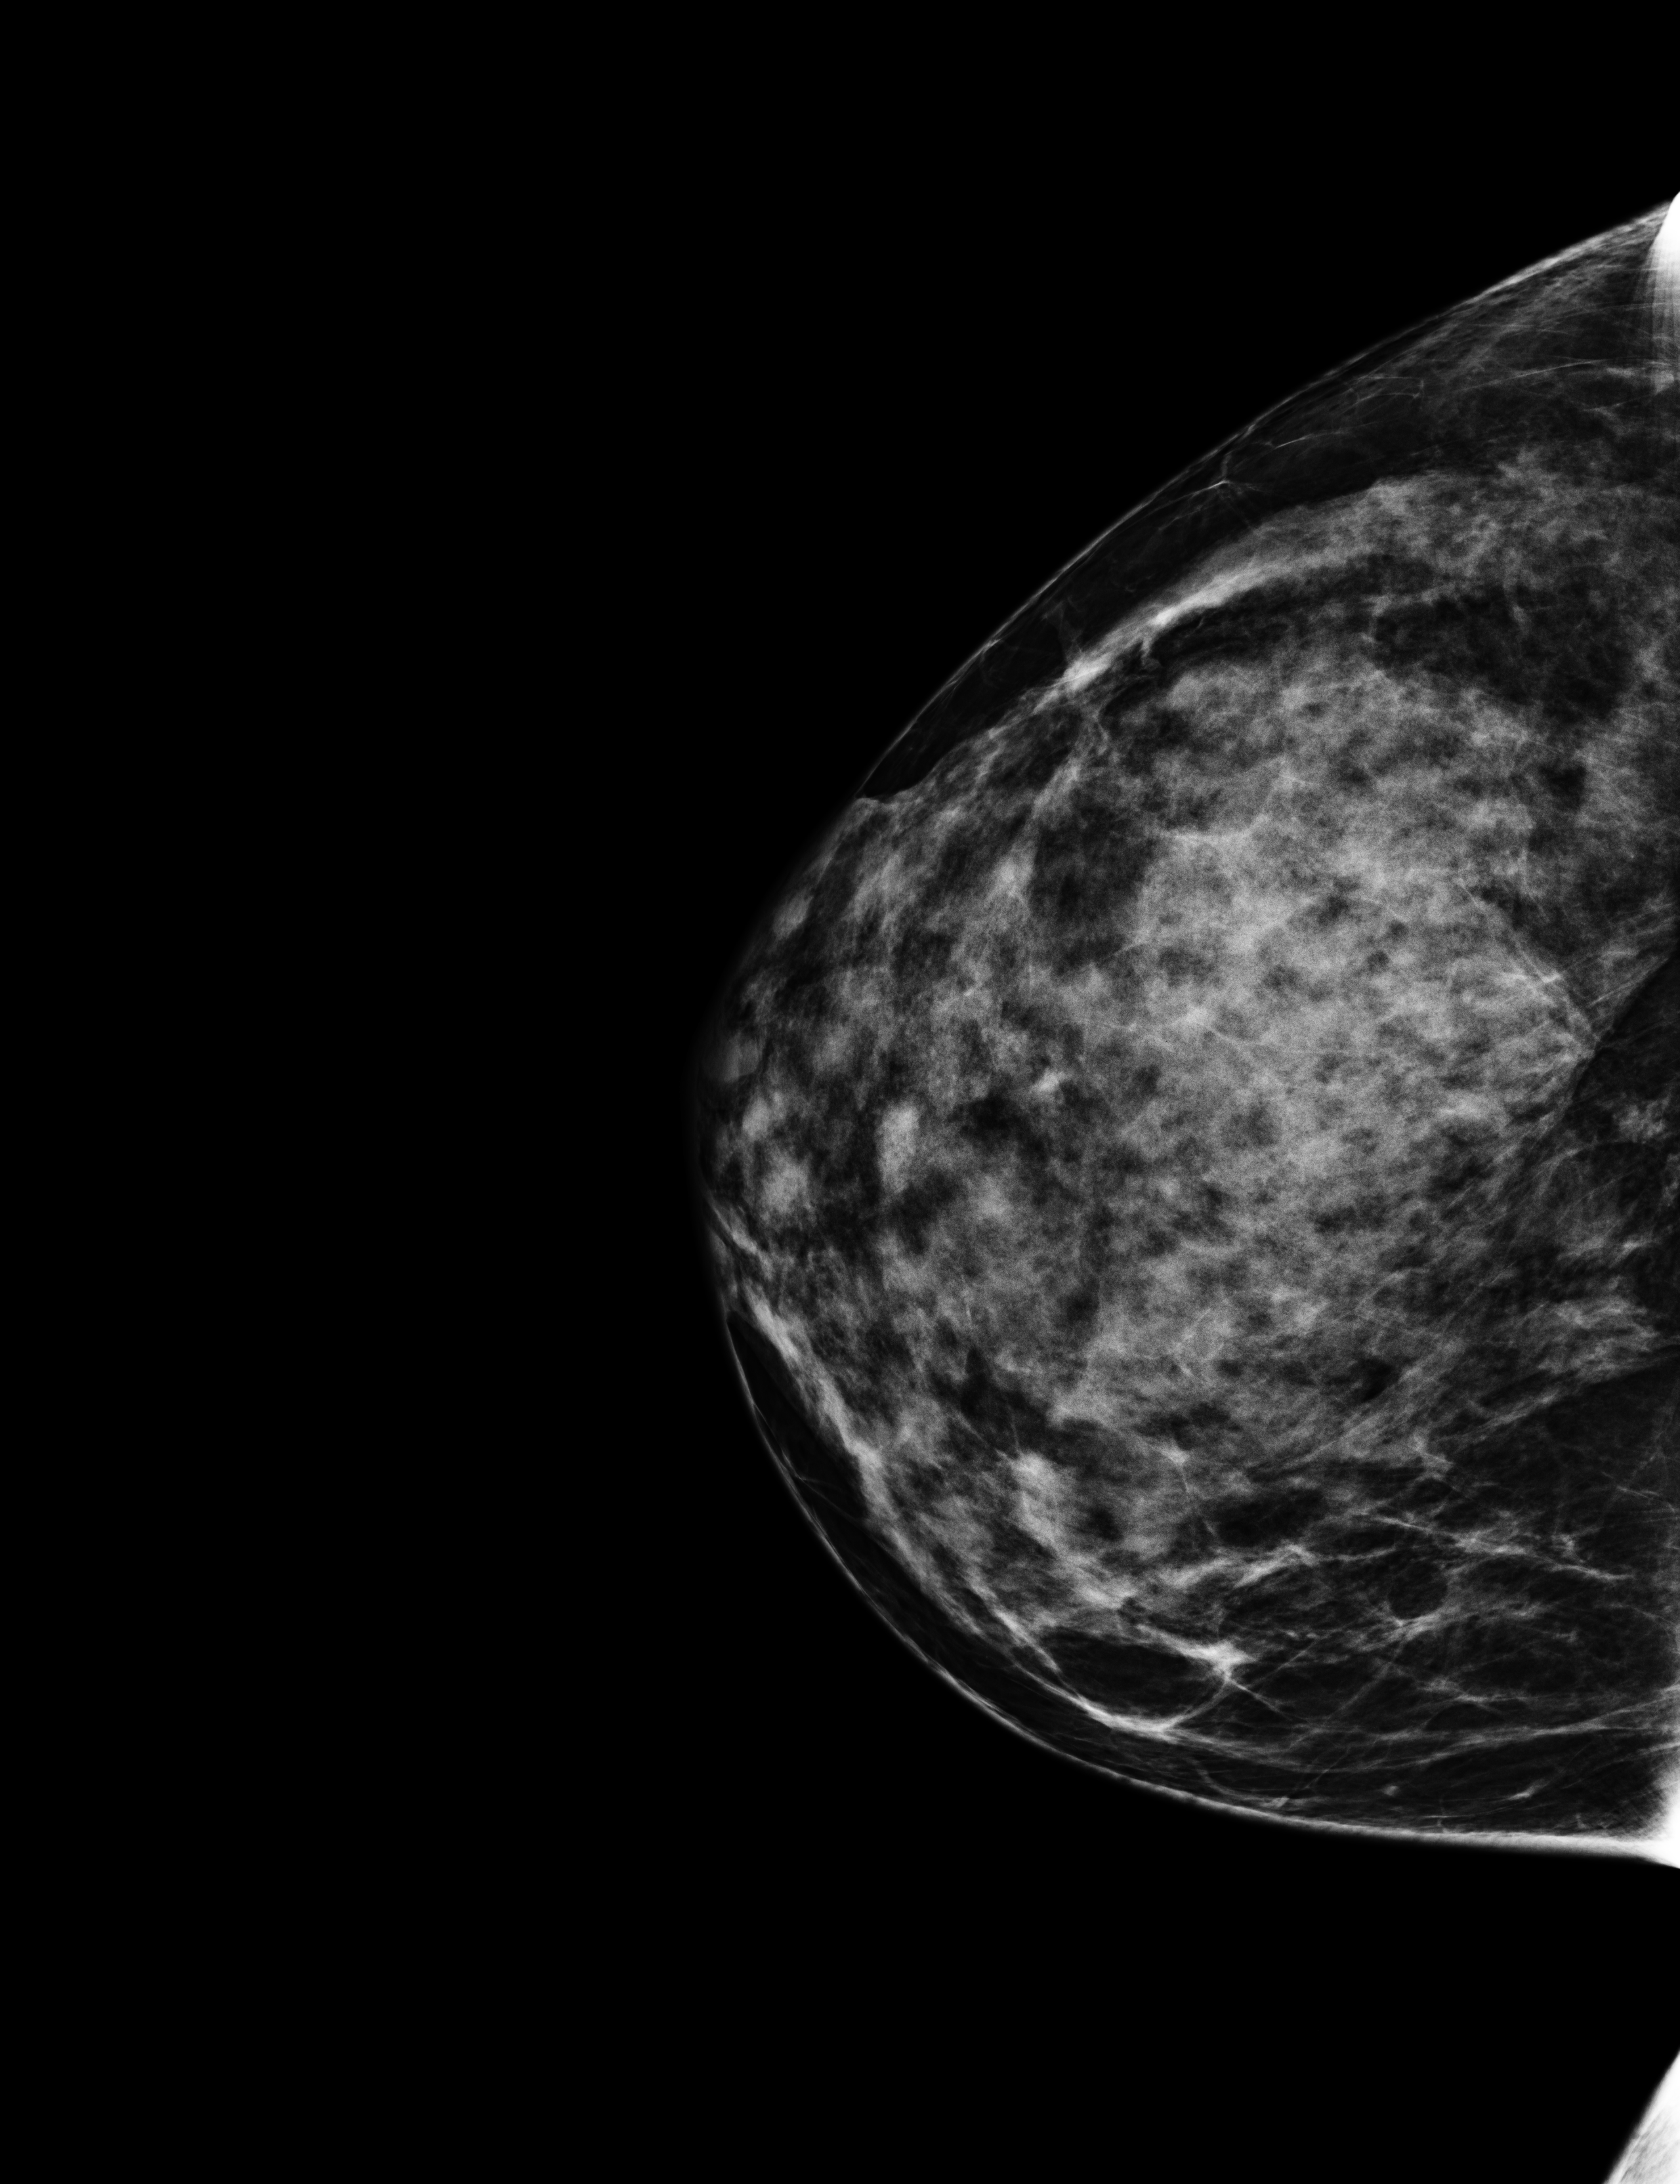
Full-field digital mammogram (FFDM); right breast; cranio-caudal projection; screening examination. Female patient, age 42 years.
Breast density at the screening exam (both breasts): extremely dense (BI-RADS density category d). Final BI-RADS category for the screening round (tomosynthesis exam, both breasts): category 1. Recall: no recall after this screen.